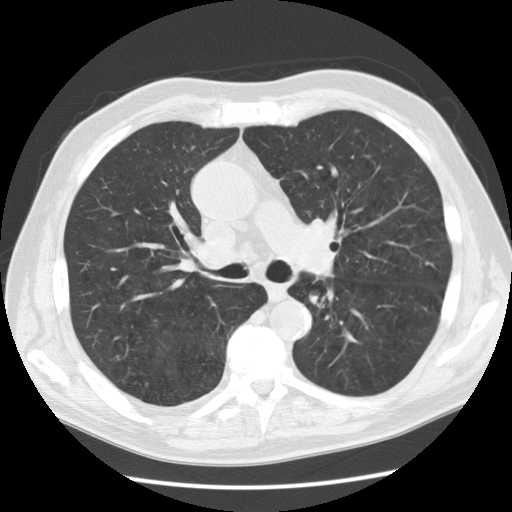
Chest CT (low-dose screening protocol), one axial image; second screening round (one year after baseline); lung window (W 1500 / L -600 HU); standard (soft-tissue) reconstruction kernel (STANDARD). Male participant, aged 73 years at enrolment.
Lesion marked by an expert reader, bounding box <293,276,338,317> (left, top, right, bottom; pixels). The screening reader recorded 4 non-calcified nodules or masses ≥4 mm on this exam (right upper lobe, right upper lobe, left upper lobe, right lower lobe); which of them this box marks is not recorded. Official screen result: positive, no significant change: stable abnormalities potentially related to lung cancer, unchanged since the prior screening exam.